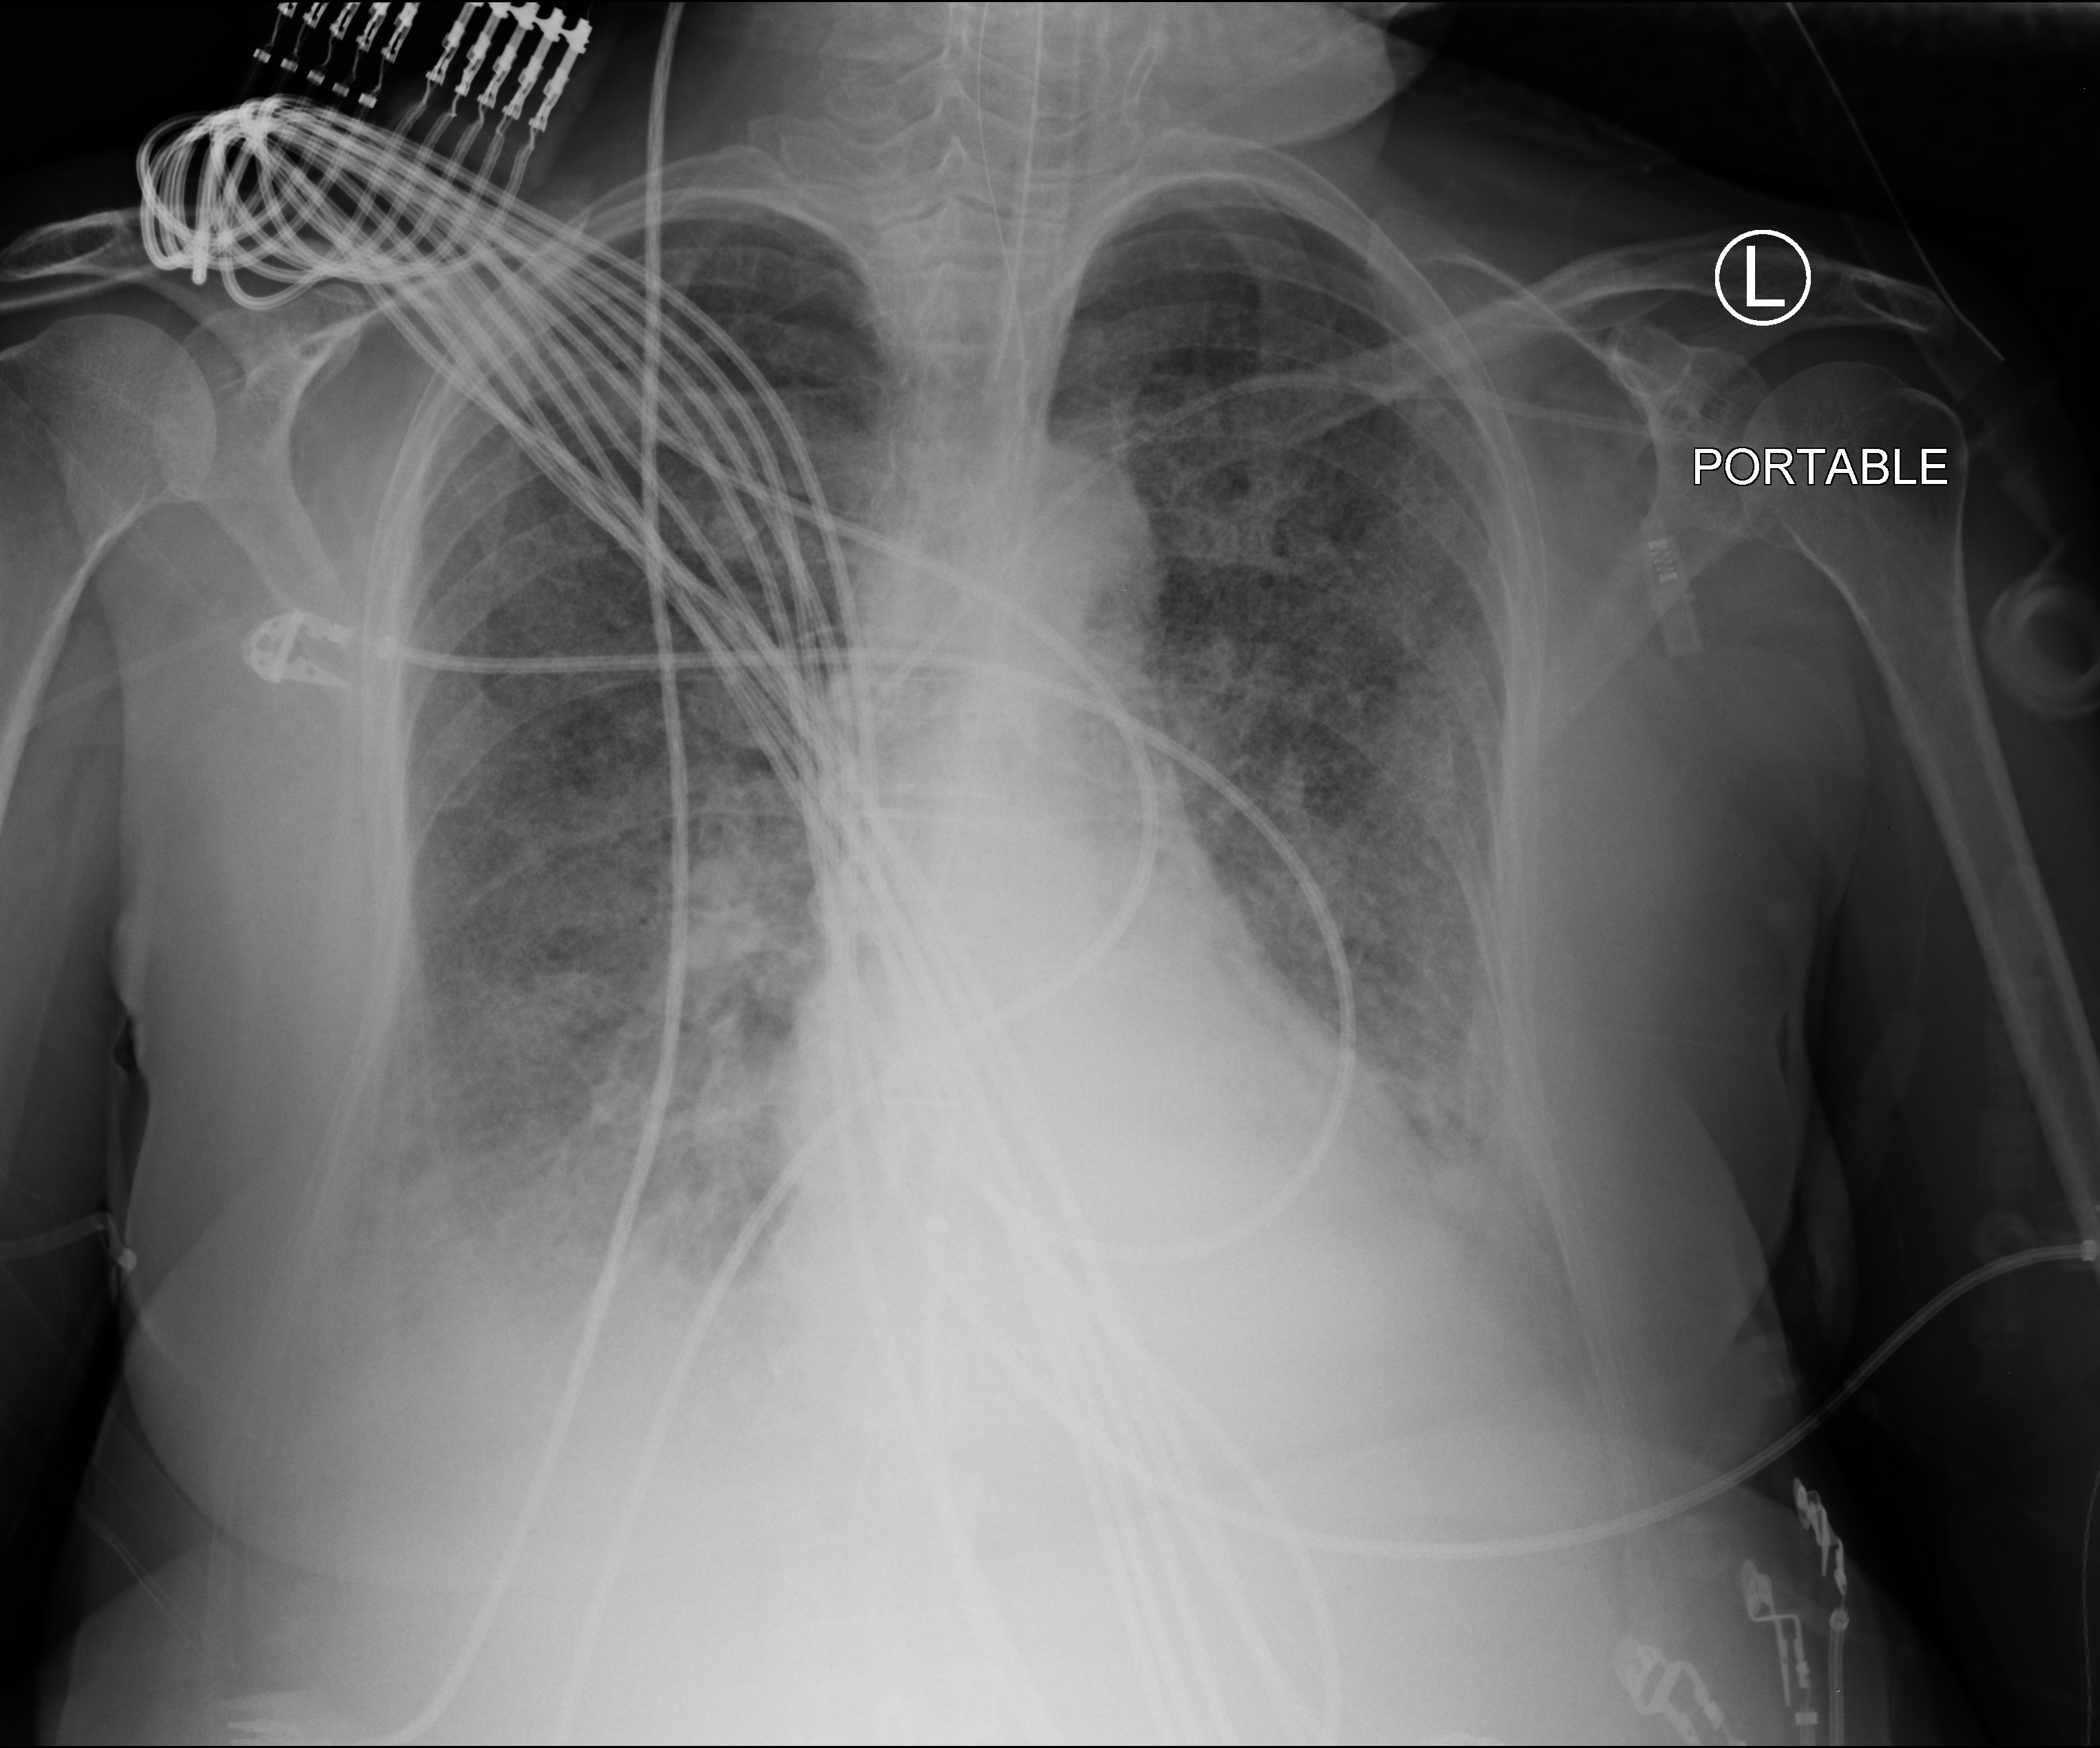
Portable chest radiograph. Female patient hospitalised with COVID-19, age 75–90 years.
From the hospital-stay record, not from the radiograph (when in the stay this image was taken is not recorded): length of hospital stay: 70 days; mechanically ventilated during this hospital stay: yes.